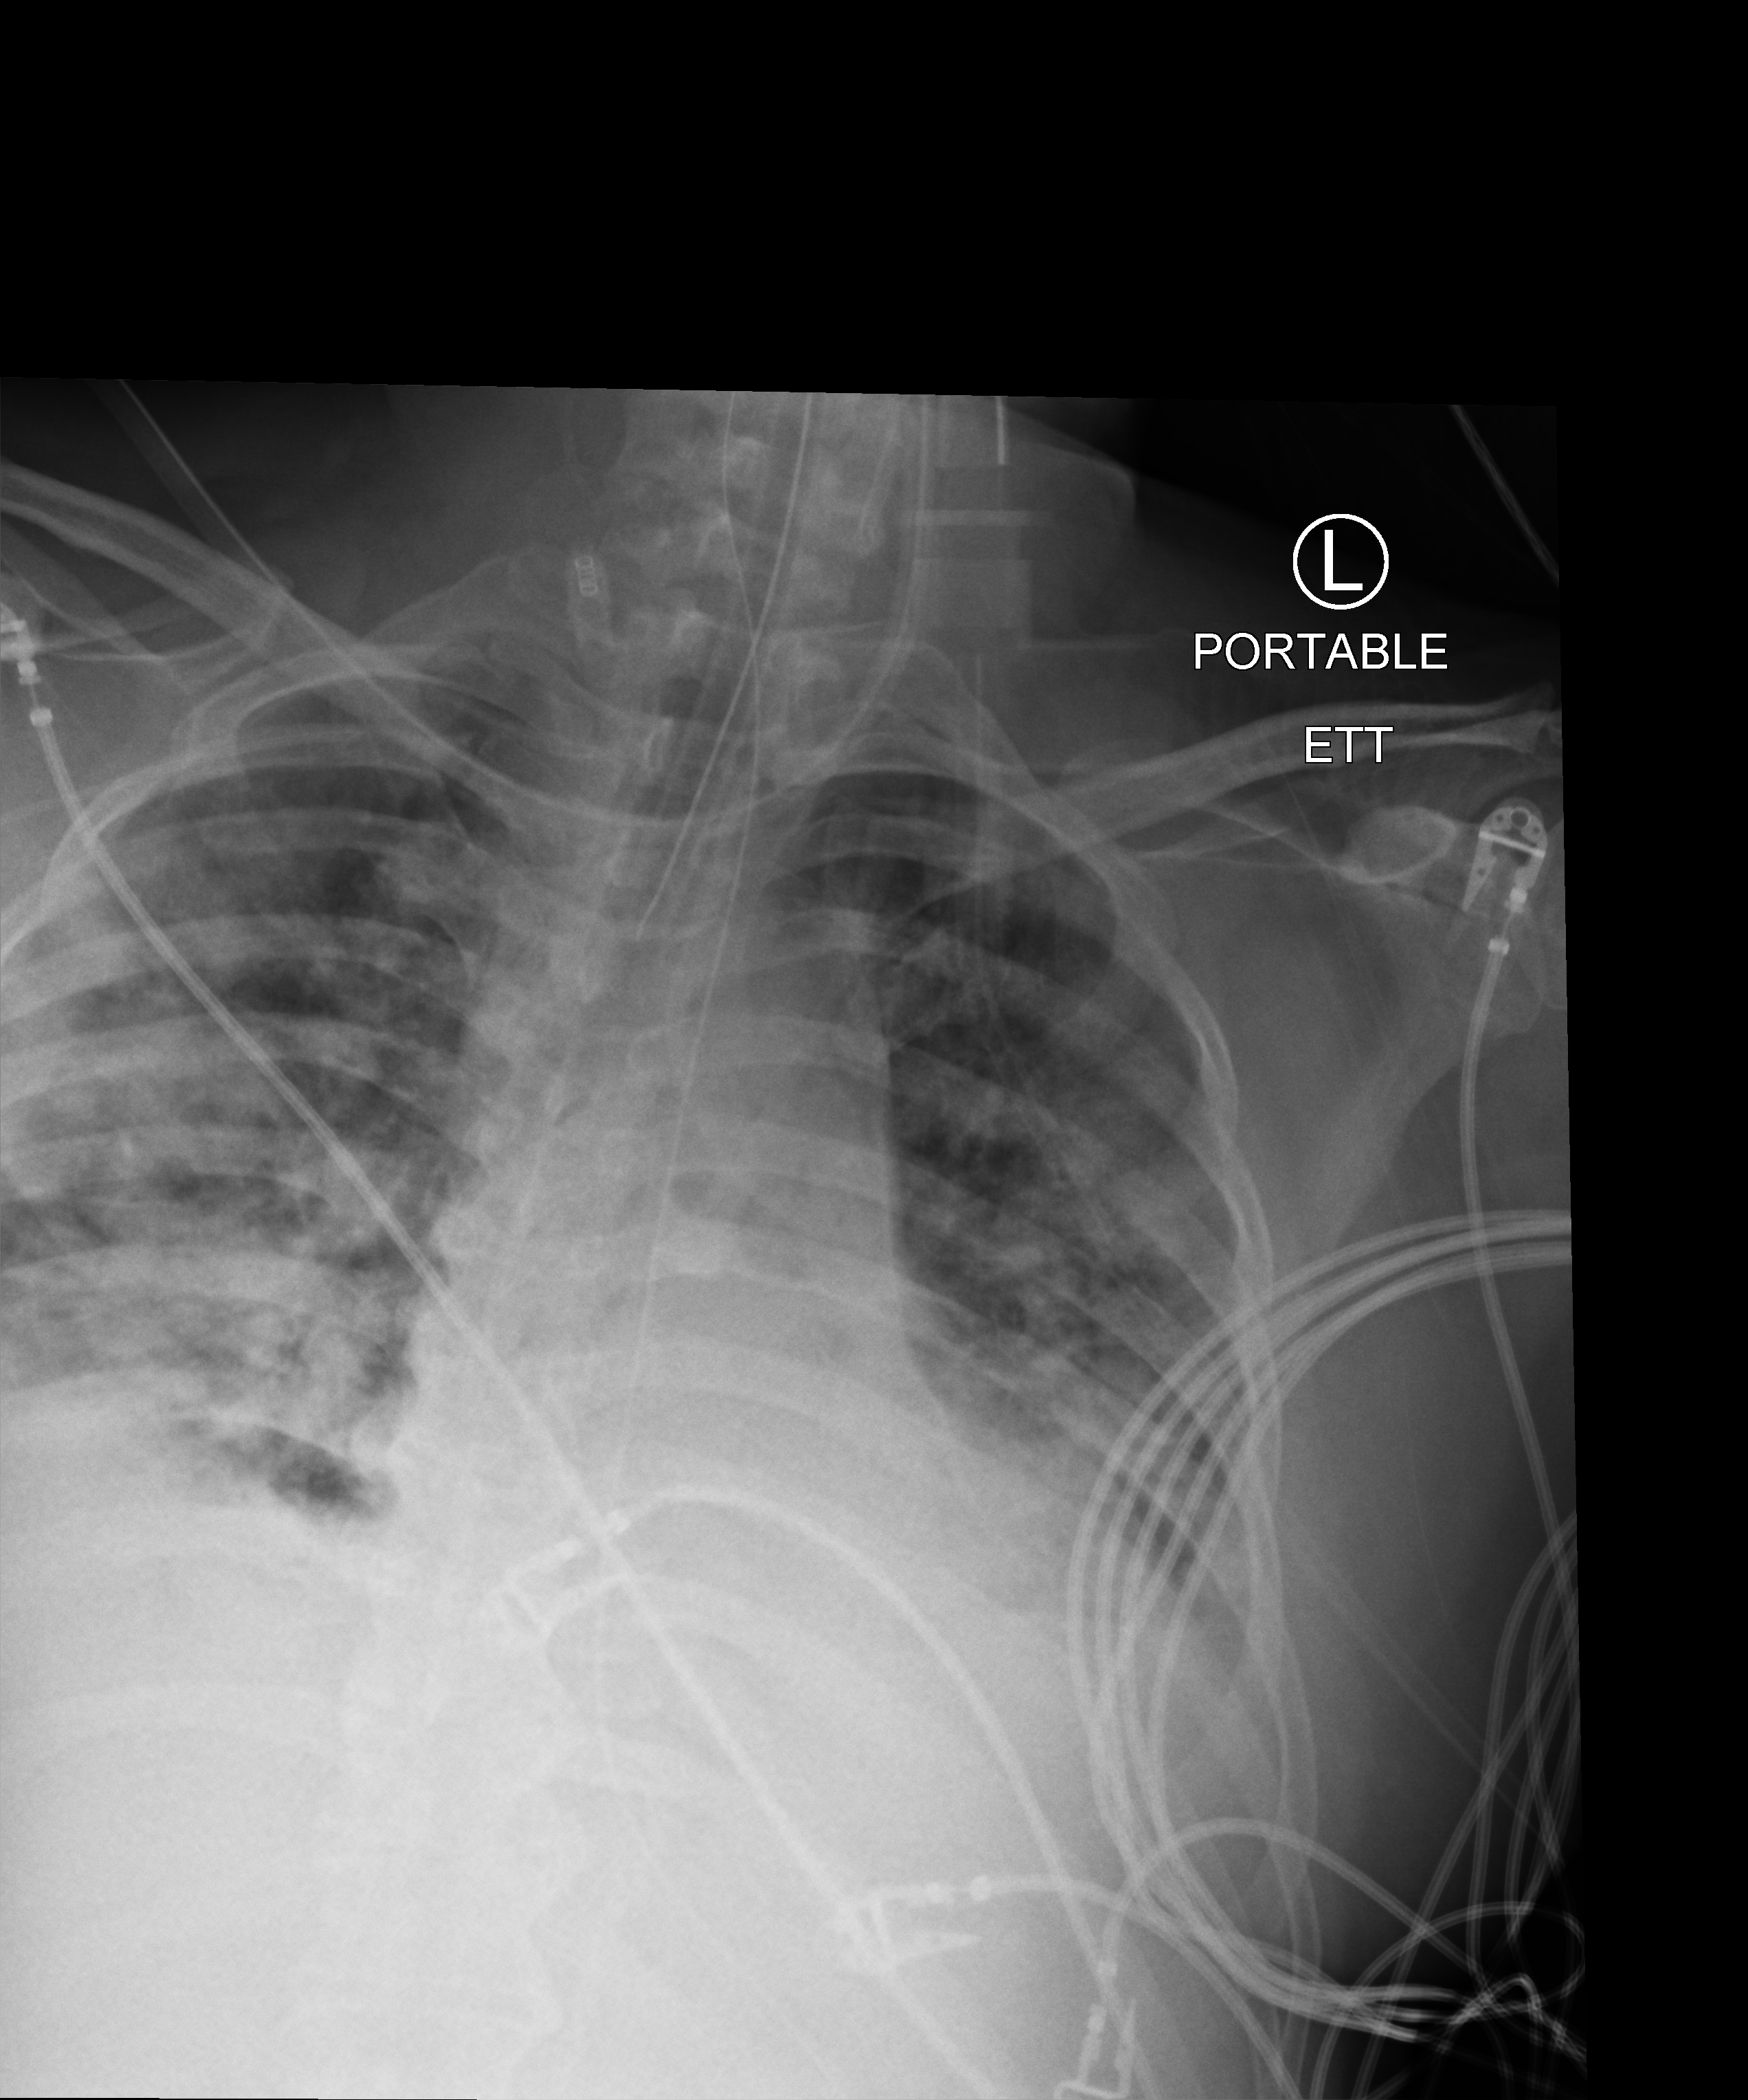
Bedside chest radiograph (computed radiography), anteroposterior (AP) projection. Male patient hospitalised with COVID-19, age 18–59 years.
Hospital-stay facts (about this admission, not read from this image; timing relative to this image not recorded):
- mechanically ventilated during this hospital stay: yes
- admitted to intensive care during this hospital stay: yes
- diabetes (admission record): yes